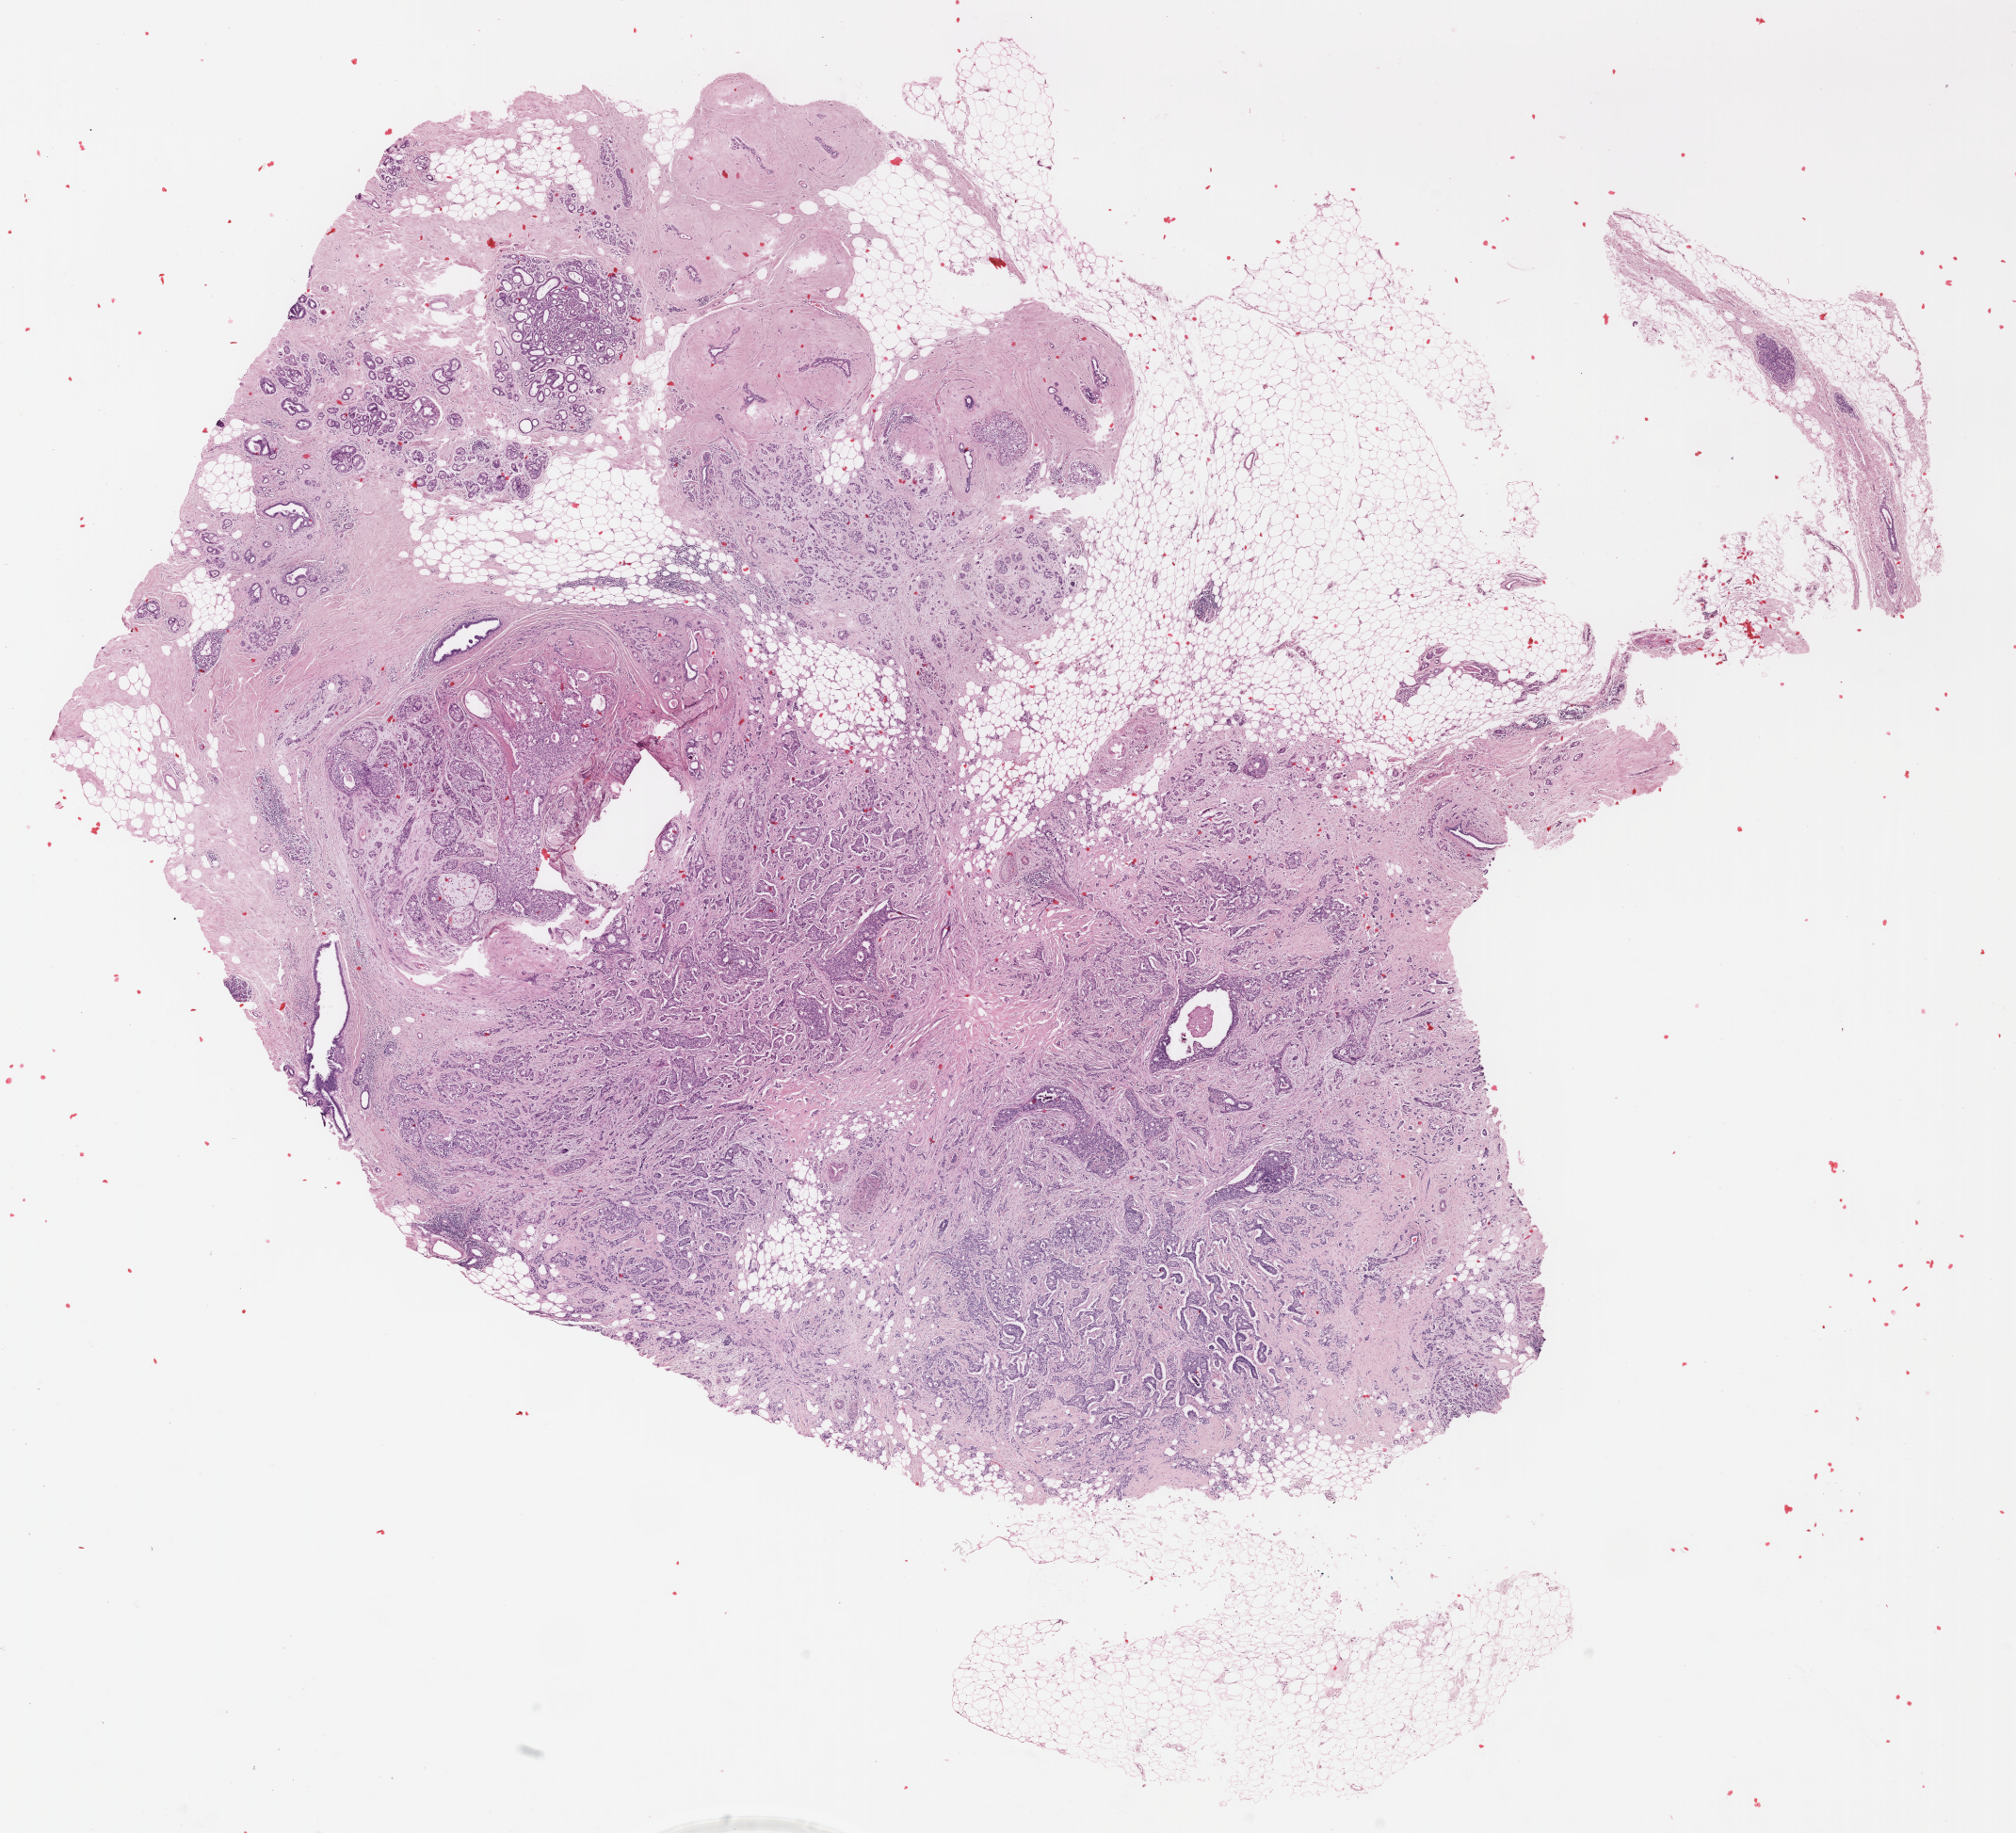
Digitized H&E tissue section (whole slide) — a low-resolution overview of the entire scanned area, about 17.0 x 15.5 mm (from a 40x scan), FFPE section, breast, primary tumour sample. Female, age 57 years at initial diagnosis.
• laterality: right
• lymph nodes positive (case pathology): 0 of 11 examined
• diagnosis: Infiltrating duct carcinoma, NOS
• AJCC pathologic stage: IIA (7th edition)